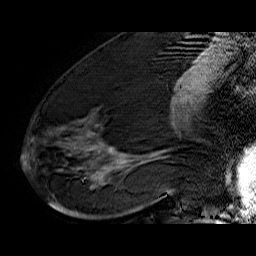
Breast MRI (dynamic contrast-enhanced), one sagittal slice; position 29 of 60 along the scan axis; dynamic contrast-enhanced series, time point 2 of 6 at this slice position (early post-contrast); 1.5 T; TE 6.4 ms, TR 32.9 ms; 256 × 256 image matrix. Female patient. From the clinical record (not read from this slice): setting: breast cancer imaged before/during neoadjuvant chemotherapy; receptor status: HR-positive, HER2-negative.
Outlined on this slice (semi-automatic segmentation, software-assisted and operator-edited):
- analysis volume of interest (the breast-tissue region the enhancement analysis was run in; not a lesion): bounding box [x1, y1, x2, y2] px = [48, 74, 176, 210]
- tumour enhancement mask (voxels above the 100 % enhancement threshold inside the analysis volume of interest): [84, 98, 176, 182]